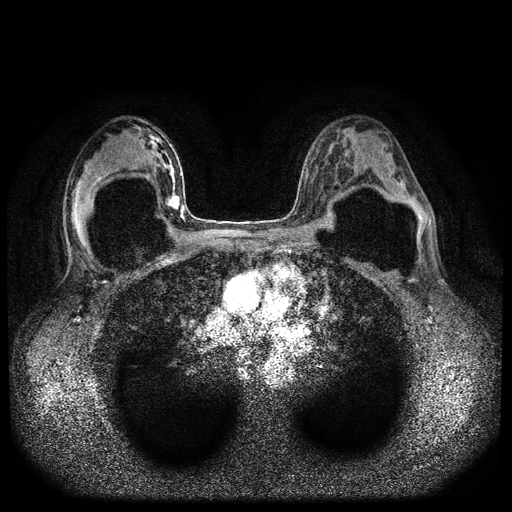
Breast MRI (dynamic contrast-enhanced, multi-phase), one axial slice. Slice 56 of 116 in the series (ordered by position). Dynamic contrast-enhanced series, time point 2 of 5 at this slice position (early post-contrast). 1.5 T. TE 2.6 ms, TR 5.4 ms. 512 × 512 image matrix, field of view 340 × 340 mm. Patient: female, 42 years.
Structures marked on this image (semi-automatically segmented with operator editing):
- breast lesion (labelled 'tumour' in the annotation; benign lesions carry a separate 'benign' label): bounding box <164,193,180,211> (left, top, right, bottom; pixels)